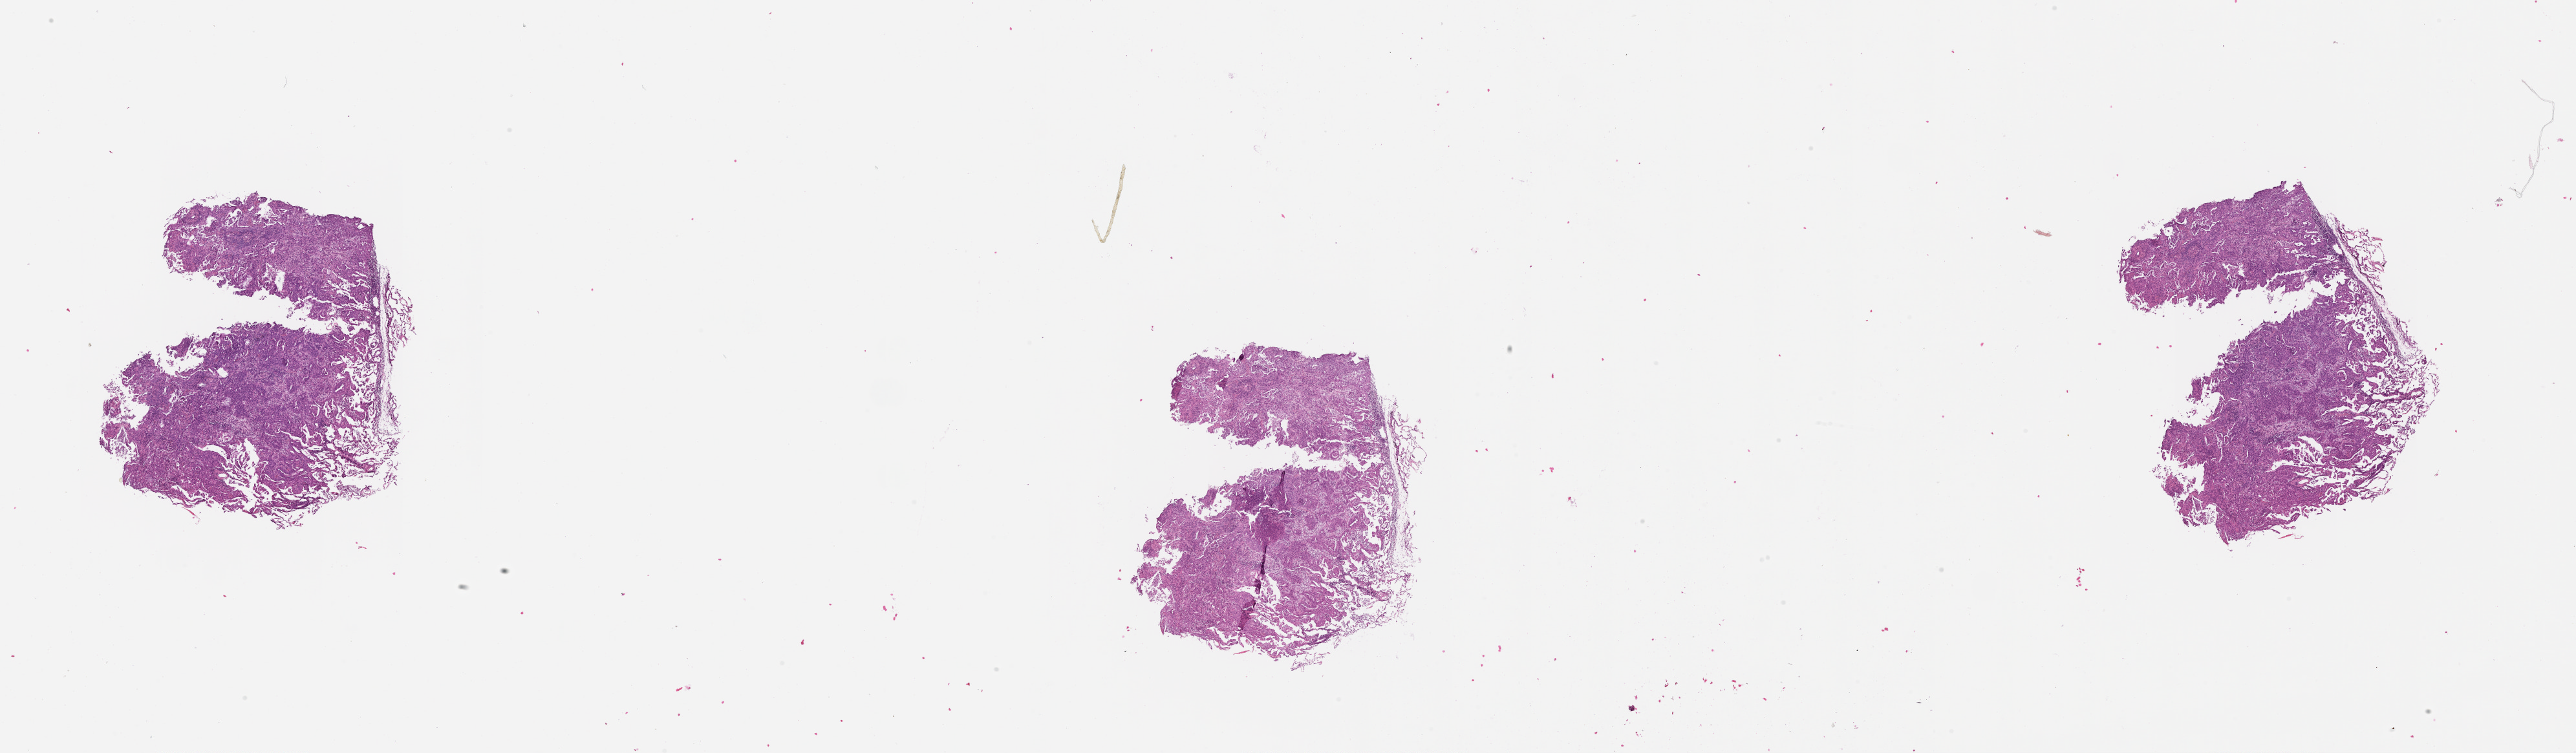
Whole-slide histology image, Hematoxylin and eosin (H&E) stained, shown as a low-resolution overview of the whole scanned area (about 32.1 x 9.4 mm, slide scanned at 20x). Tumour tissue sample, sampled site: lung. 60-year-old male patient. Histologic grade: G2 (moderately differentiated). Slide review estimates, as recorded: tumour nuclei 75%, necrosis 5%.
AJCC pathologic stage: IA. Histologic diagnosis: Adenocarcinoma, NOS. Primary tumour site (as recorded): right upper lobe.